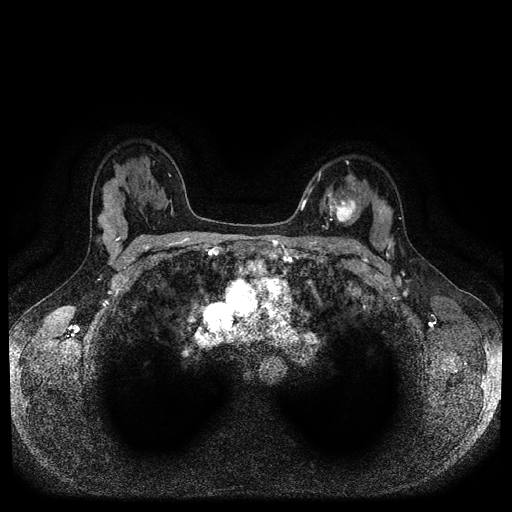
Breast MRI (dynamic contrast-enhanced, multi-phase), one axial slice; slice 70 of 116 in the series (ordered by position); dynamic contrast-enhanced series, time point 2 of 5 at this slice position (early post-contrast); 1.5 T; TE 2.6 ms, TR 5.3 ms; 2 mm slice thickness; 512 × 512 image matrix. Female patient, age 33 years.
Annotated regions visible in this slice (semi-automatic segmentation, software-assisted and operator-edited):
- breast lesion (labelled 'tumour' in the annotation; benign lesions carry a separate 'benign' label): bounding box (x1, y1, x2, y2) in pixels: (333, 196, 359, 224)